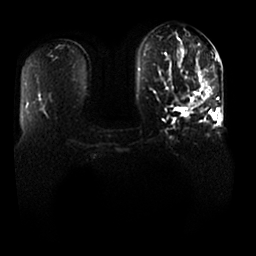
Breast MRI, one axial slice; diffusion-weighted series; image 2 of 4 stored at this slice position (different b-values; order by instance number); 1.5 T; 4 mm slice thickness; 256 × 256 image matrix, field of view 370 × 370 mm. Female patient.
Structures marked on this image (outlined manually by an expert reader):
- tumour on diffusion-weighted imaging: box from (x=182, y=93) to (x=208, y=107) px